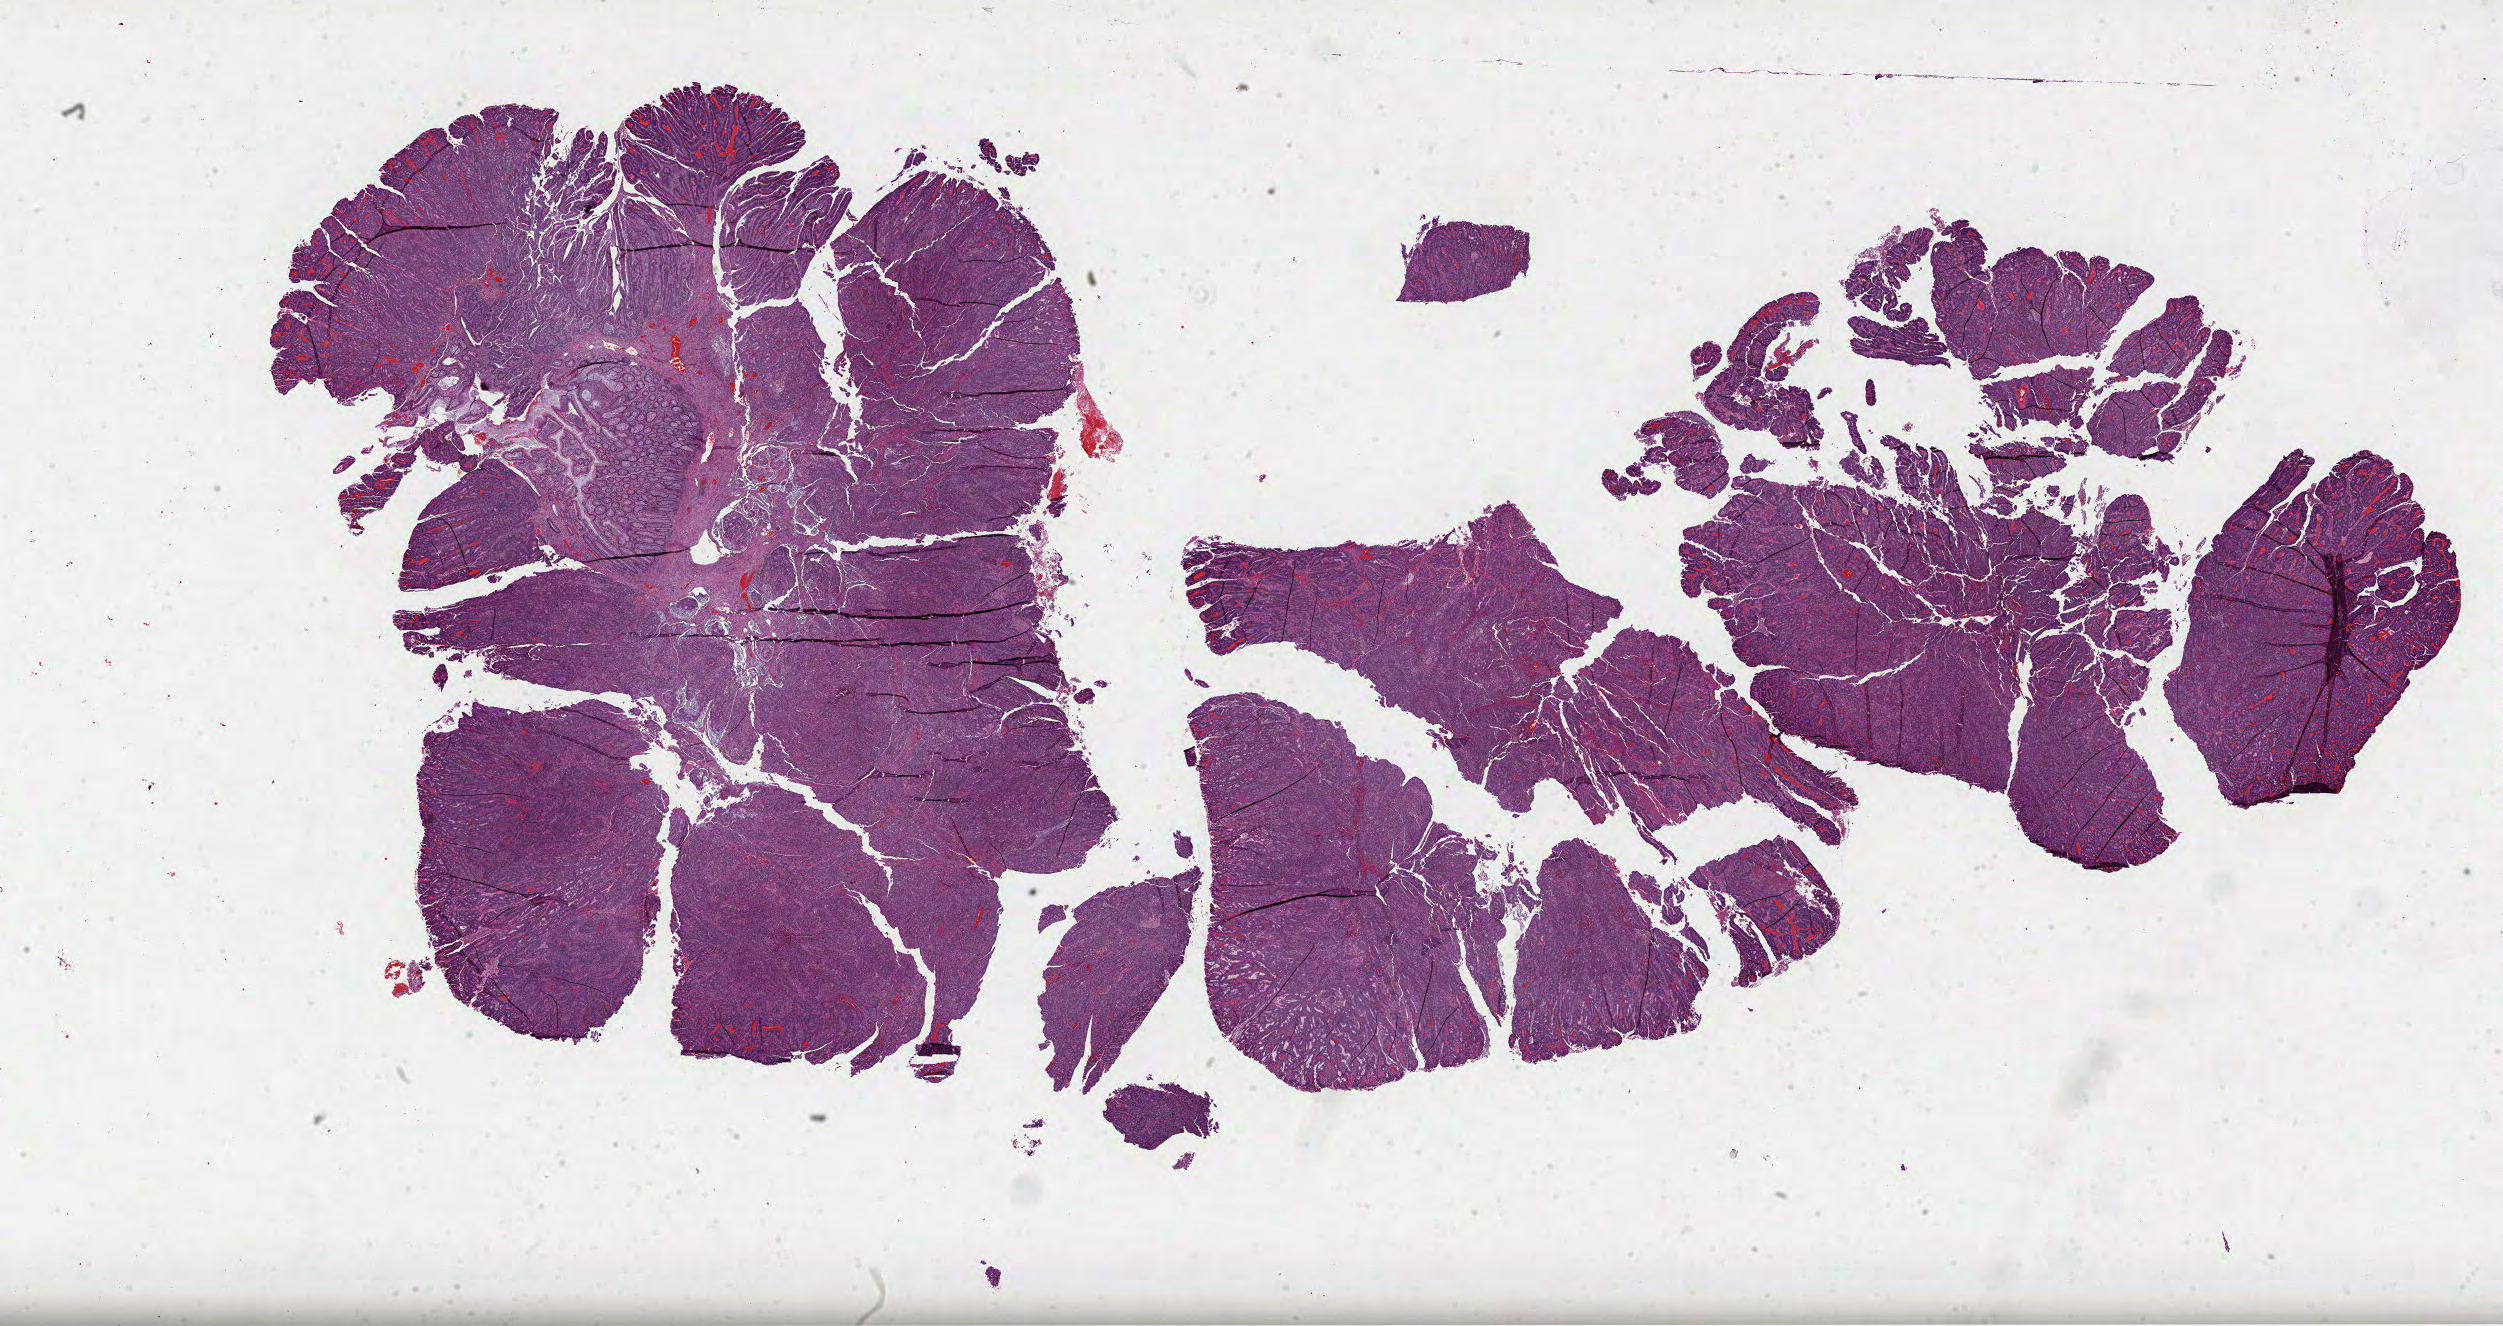
Whole-slide histology image, H&E — a low-resolution overview of the entire scanned area, about 40.4 x 21.4 mm (acquisition: 40x scan). FFPE section. Colon, primary tumour sample. Female, age 77 years at initial diagnosis.
- lymph nodes positive (case pathology): 0 of 28 examined
- diagnosis: Adenocarcinoma, NOS (ascending colon)
- AJCC pathologic stage: I (7th edition)